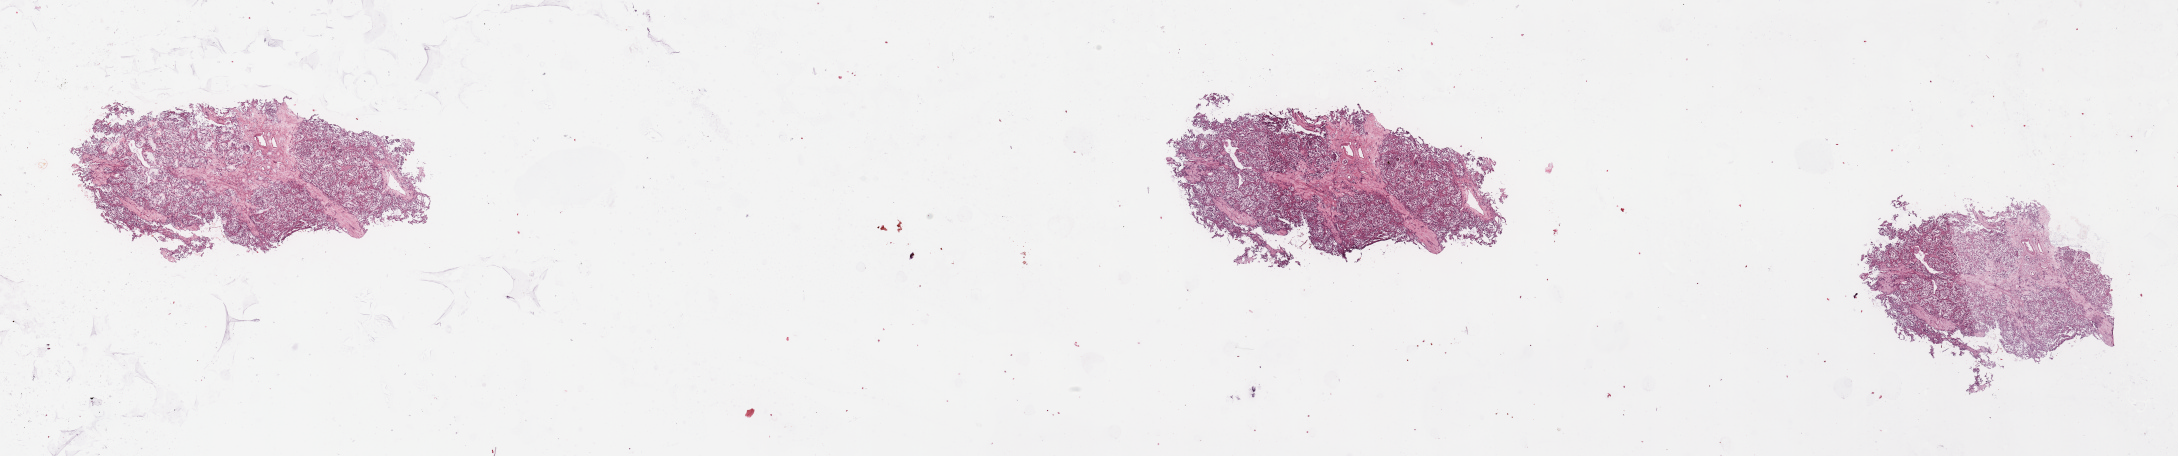
Whole-slide histology image, H&E-stained, shown as a low-resolution overview of the whole scanned area (about 34.5 x 7.2 mm); tumour tissue sample, kidney. 51-year-old male patient.
Diagnosis: Renal cell carcinoma, NOS.